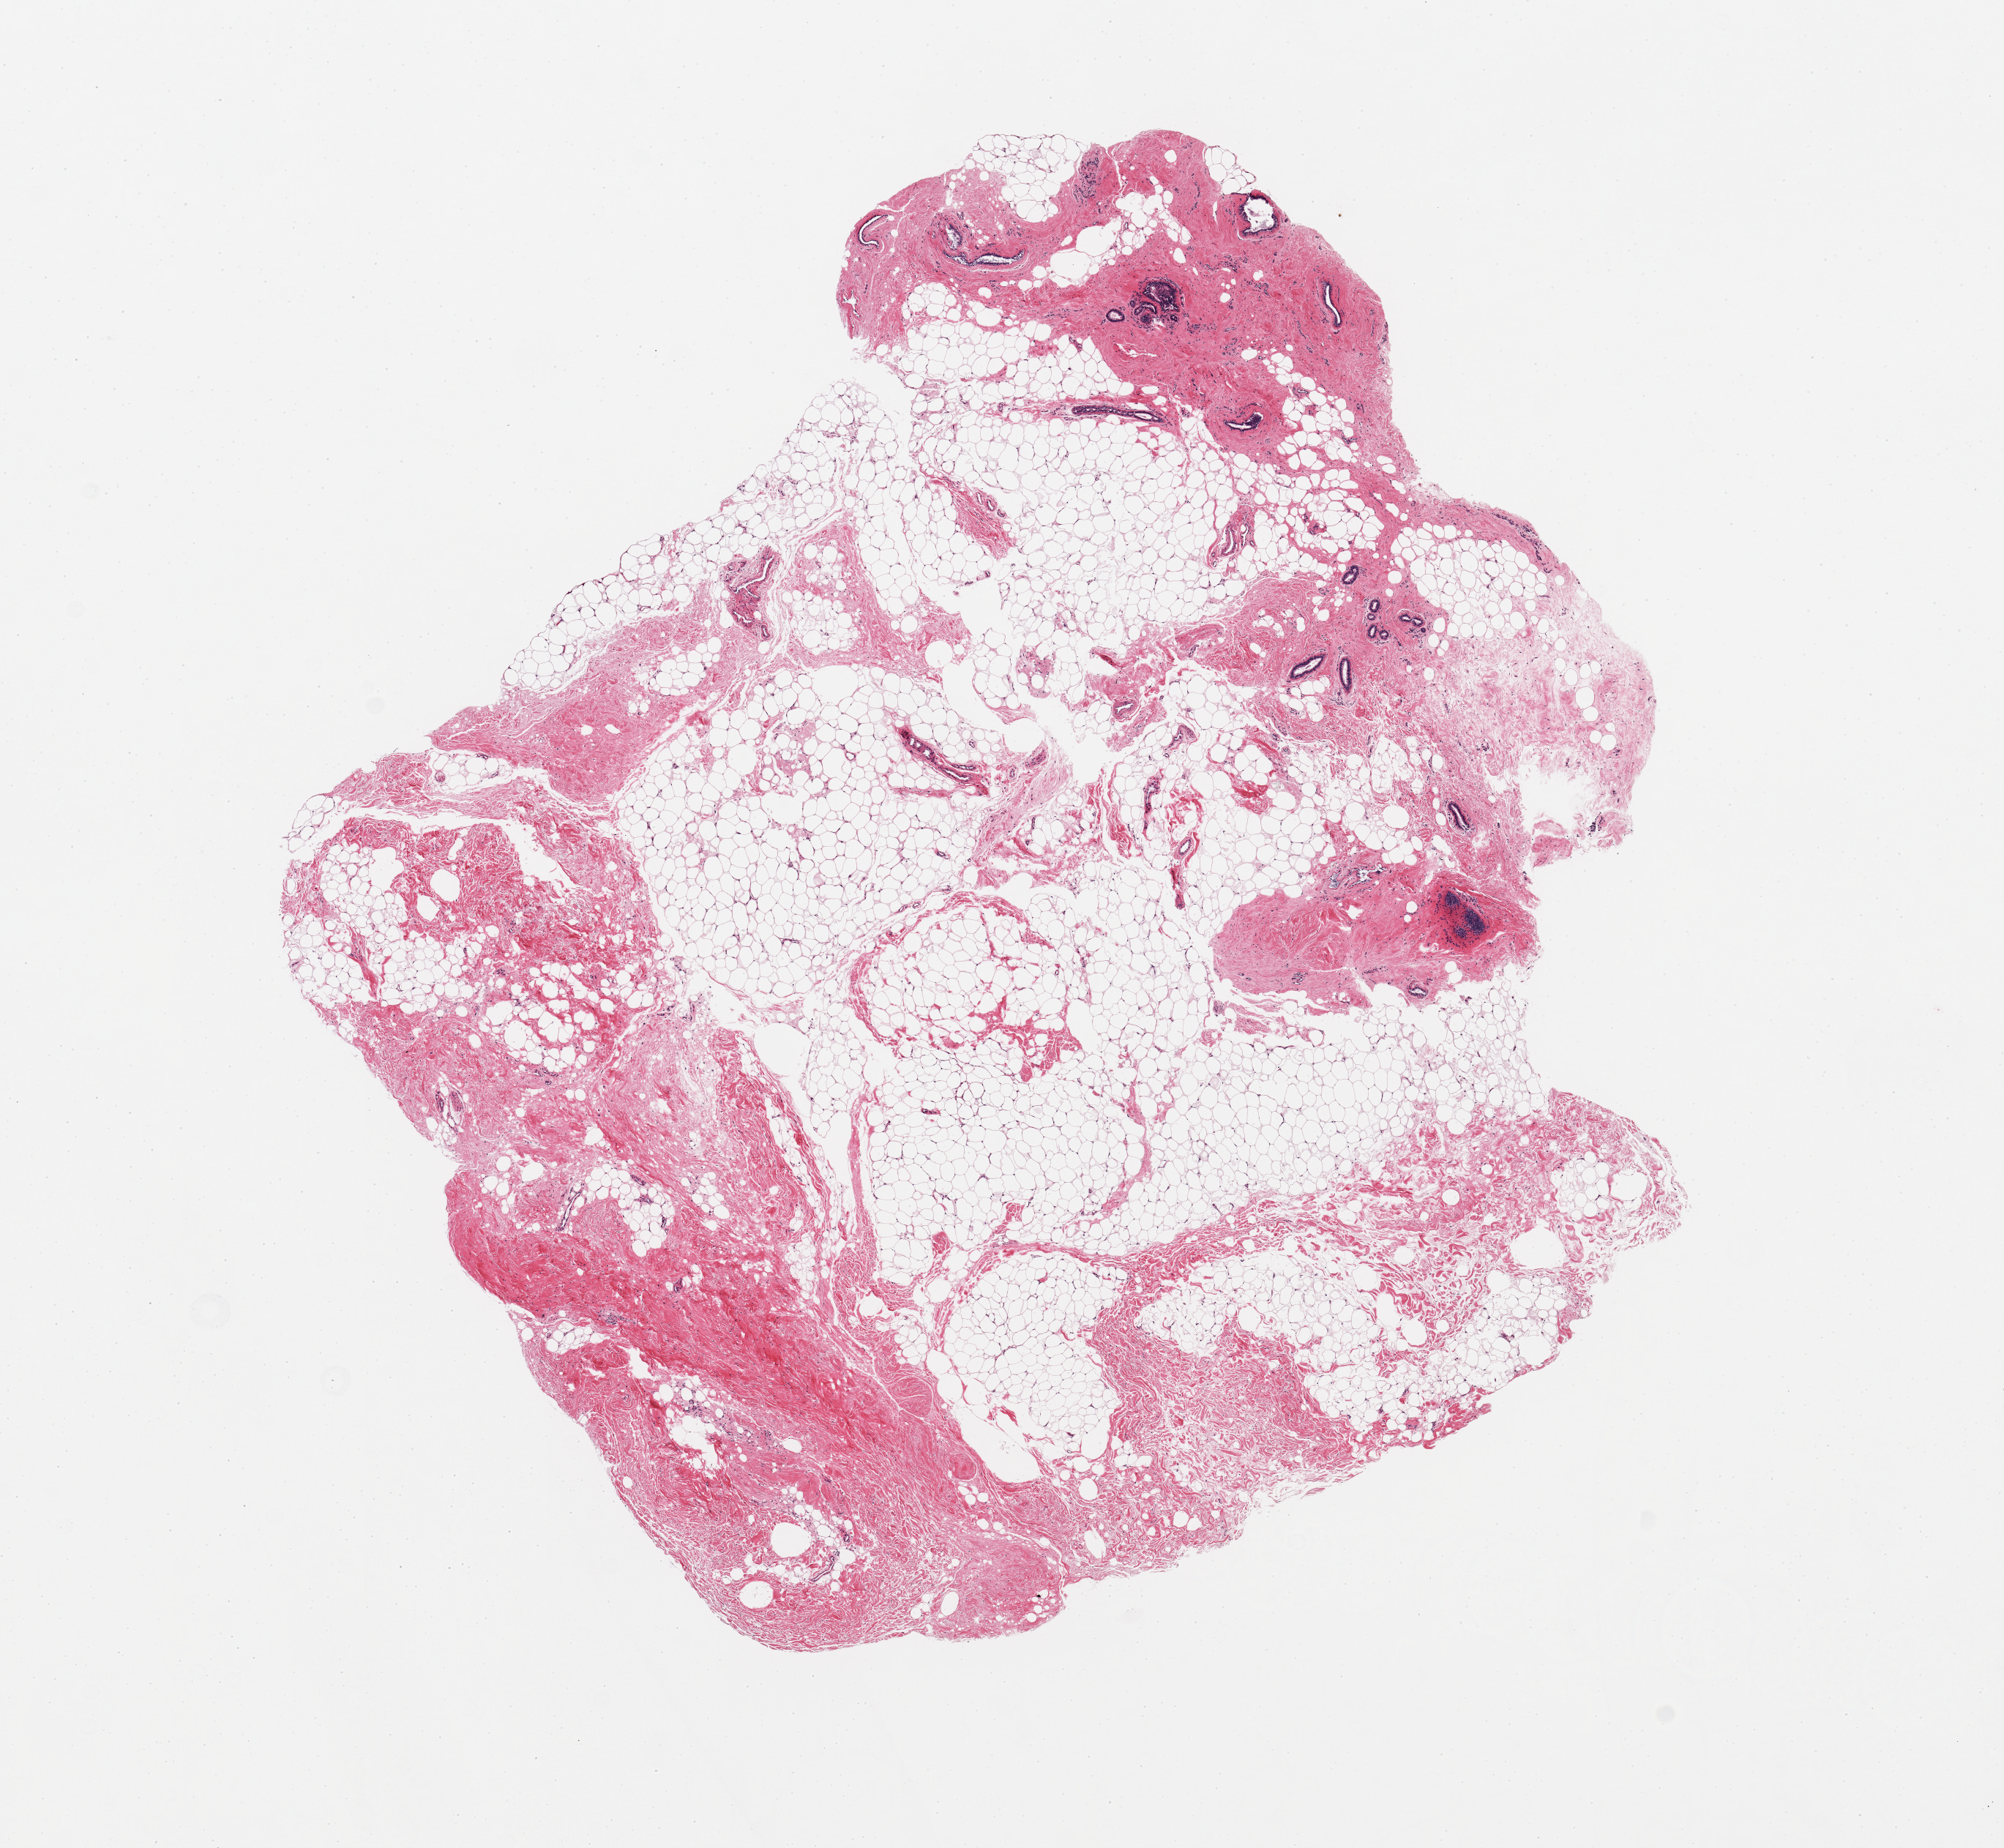
Haematoxylin and eosin whole-slide image — whole scanned area (about 10.8 x 10.0 mm, slide scanned at 20x) shown as a low-resolution overview; PAXgene-fixed paraffin-embedded (PFPE) section; sampled site (target tissue): breast; tissue donor sample. Donor: male.
Pathologist's review note for this sample: 1 piece,mainly fibroadipose elements; mild gyynecomastoid hyerplasia; ducta elements.